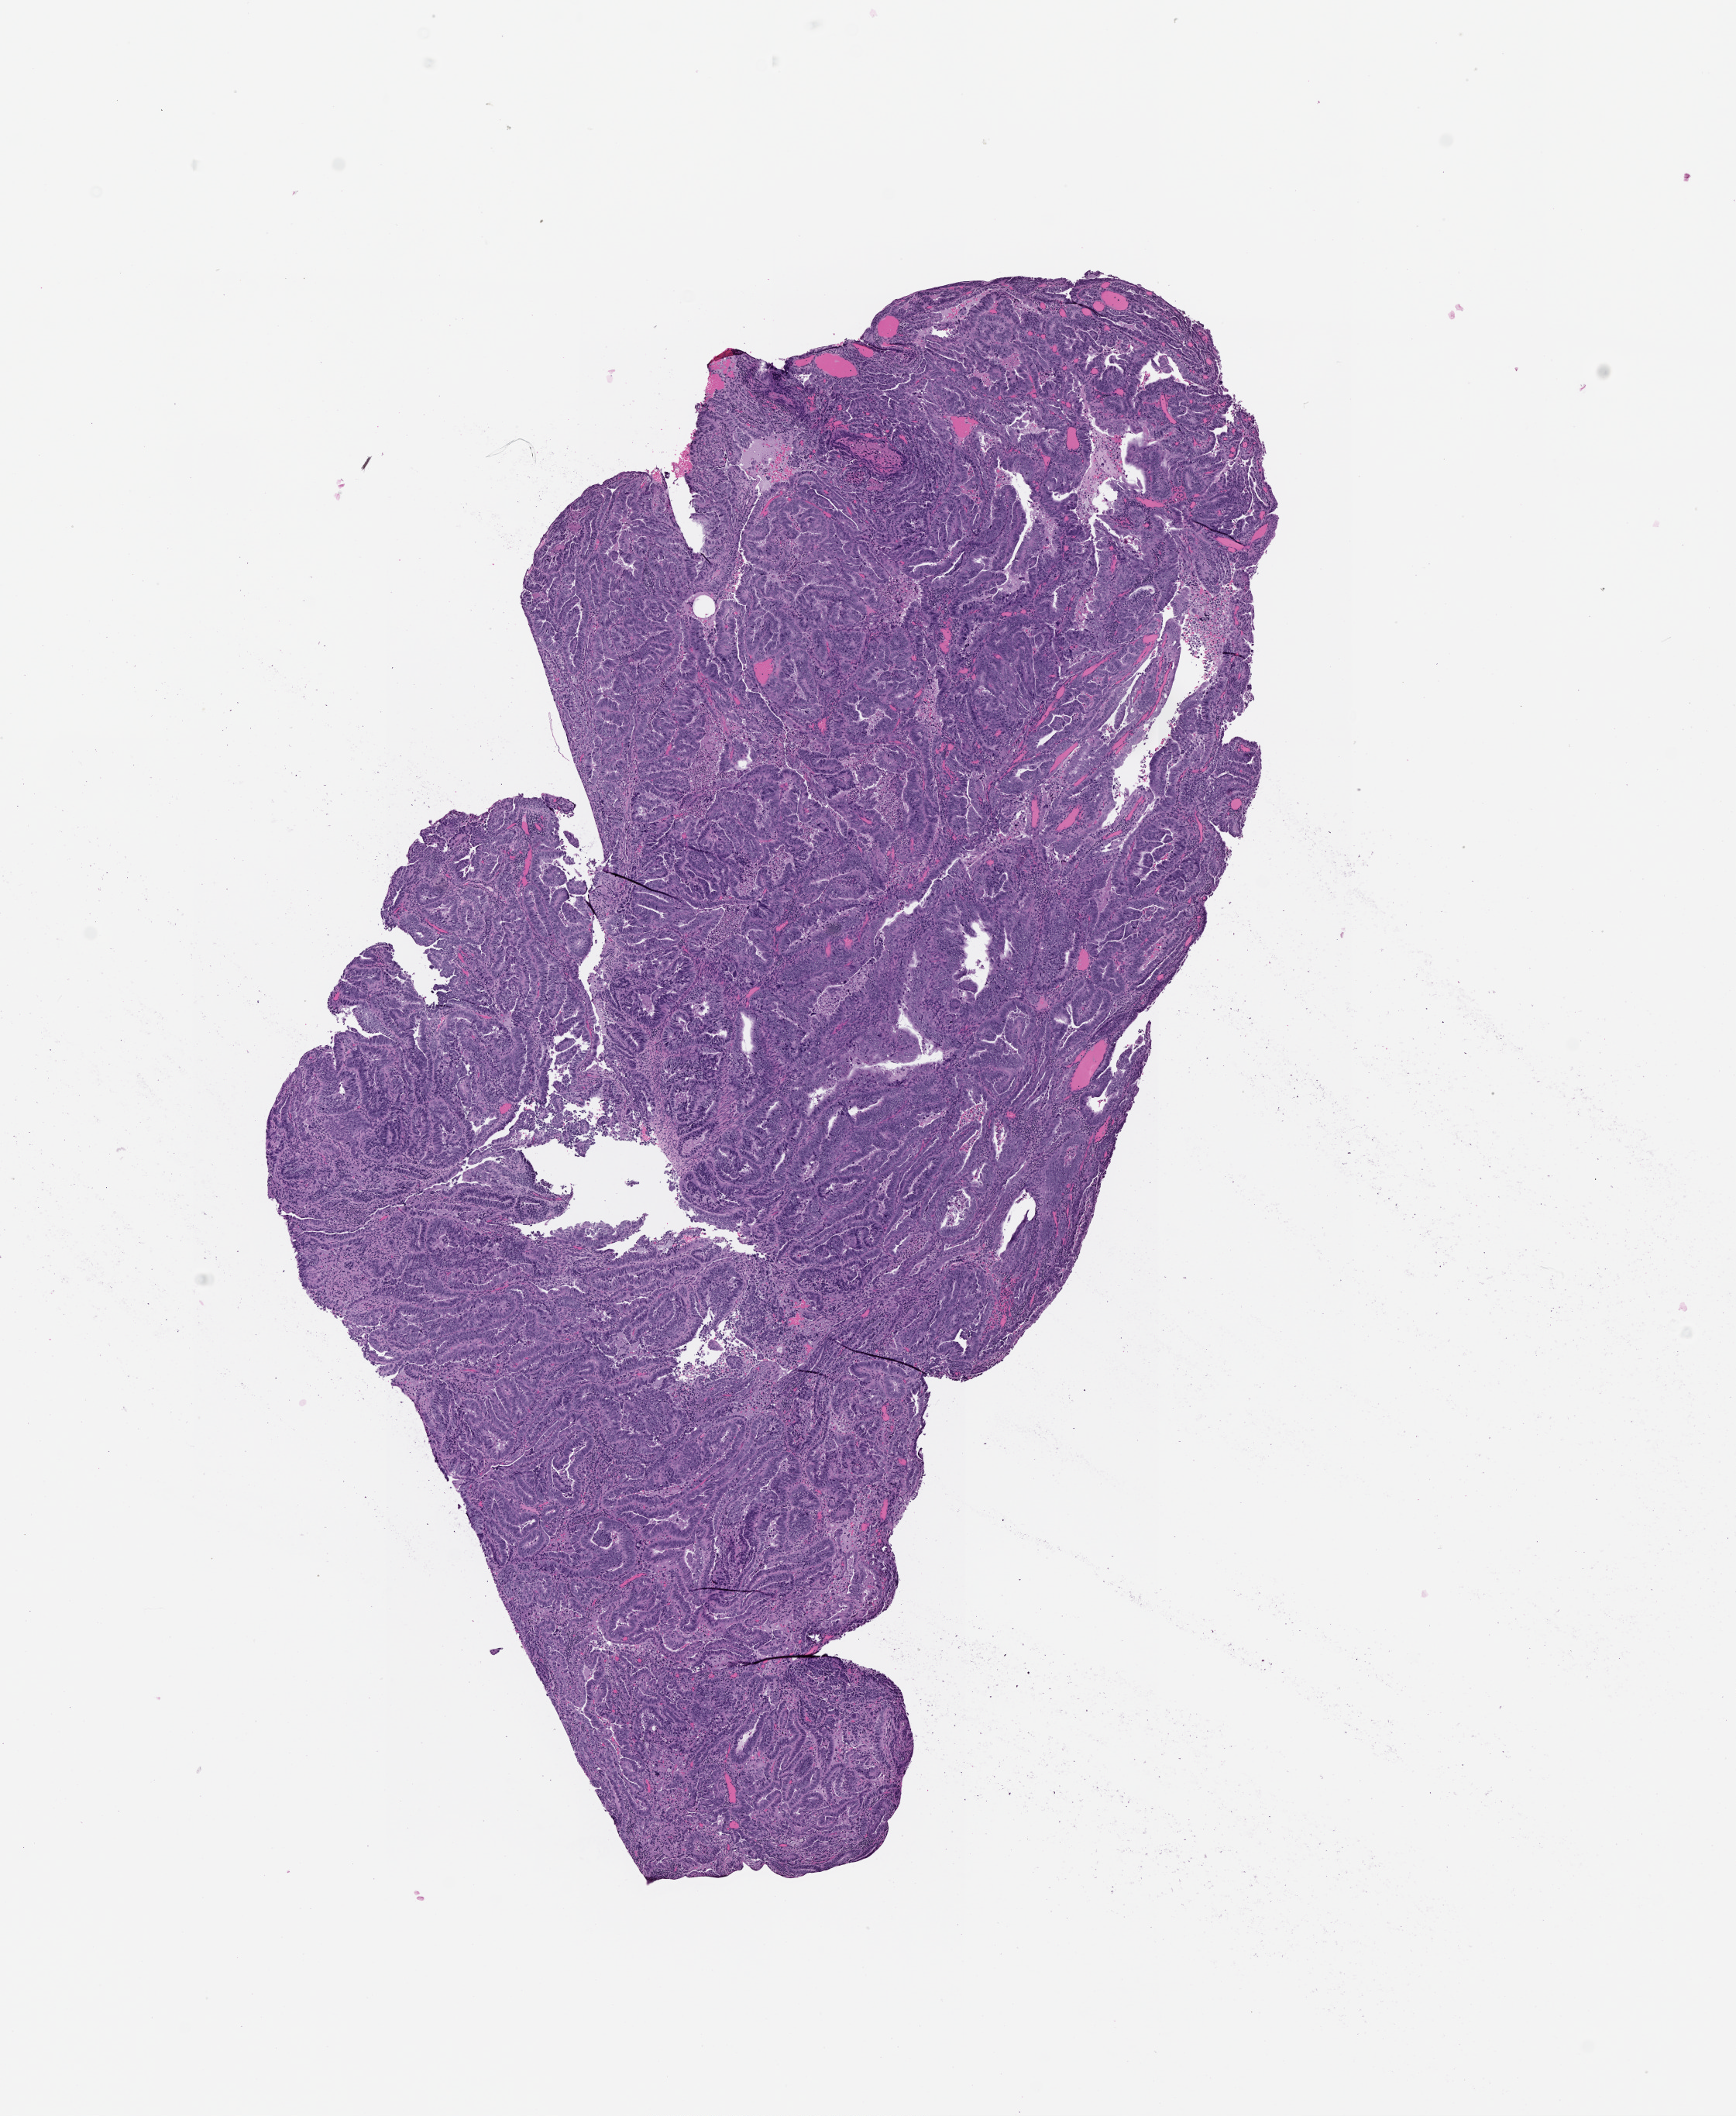
Digitized H&E tissue section (whole slide) — a low-resolution overview of the entire scanned area, about 9.0 x 11.0 mm; tumour tissue sample, uterus. 58-year-old female patient. Histologic grade: G3 (poorly differentiated).
• diagnosis: Endometrioid adenocarcinoma, NOS
• primary tumour site (as recorded): posterior endometrium
• AJCC pathologic stage: IIIC1